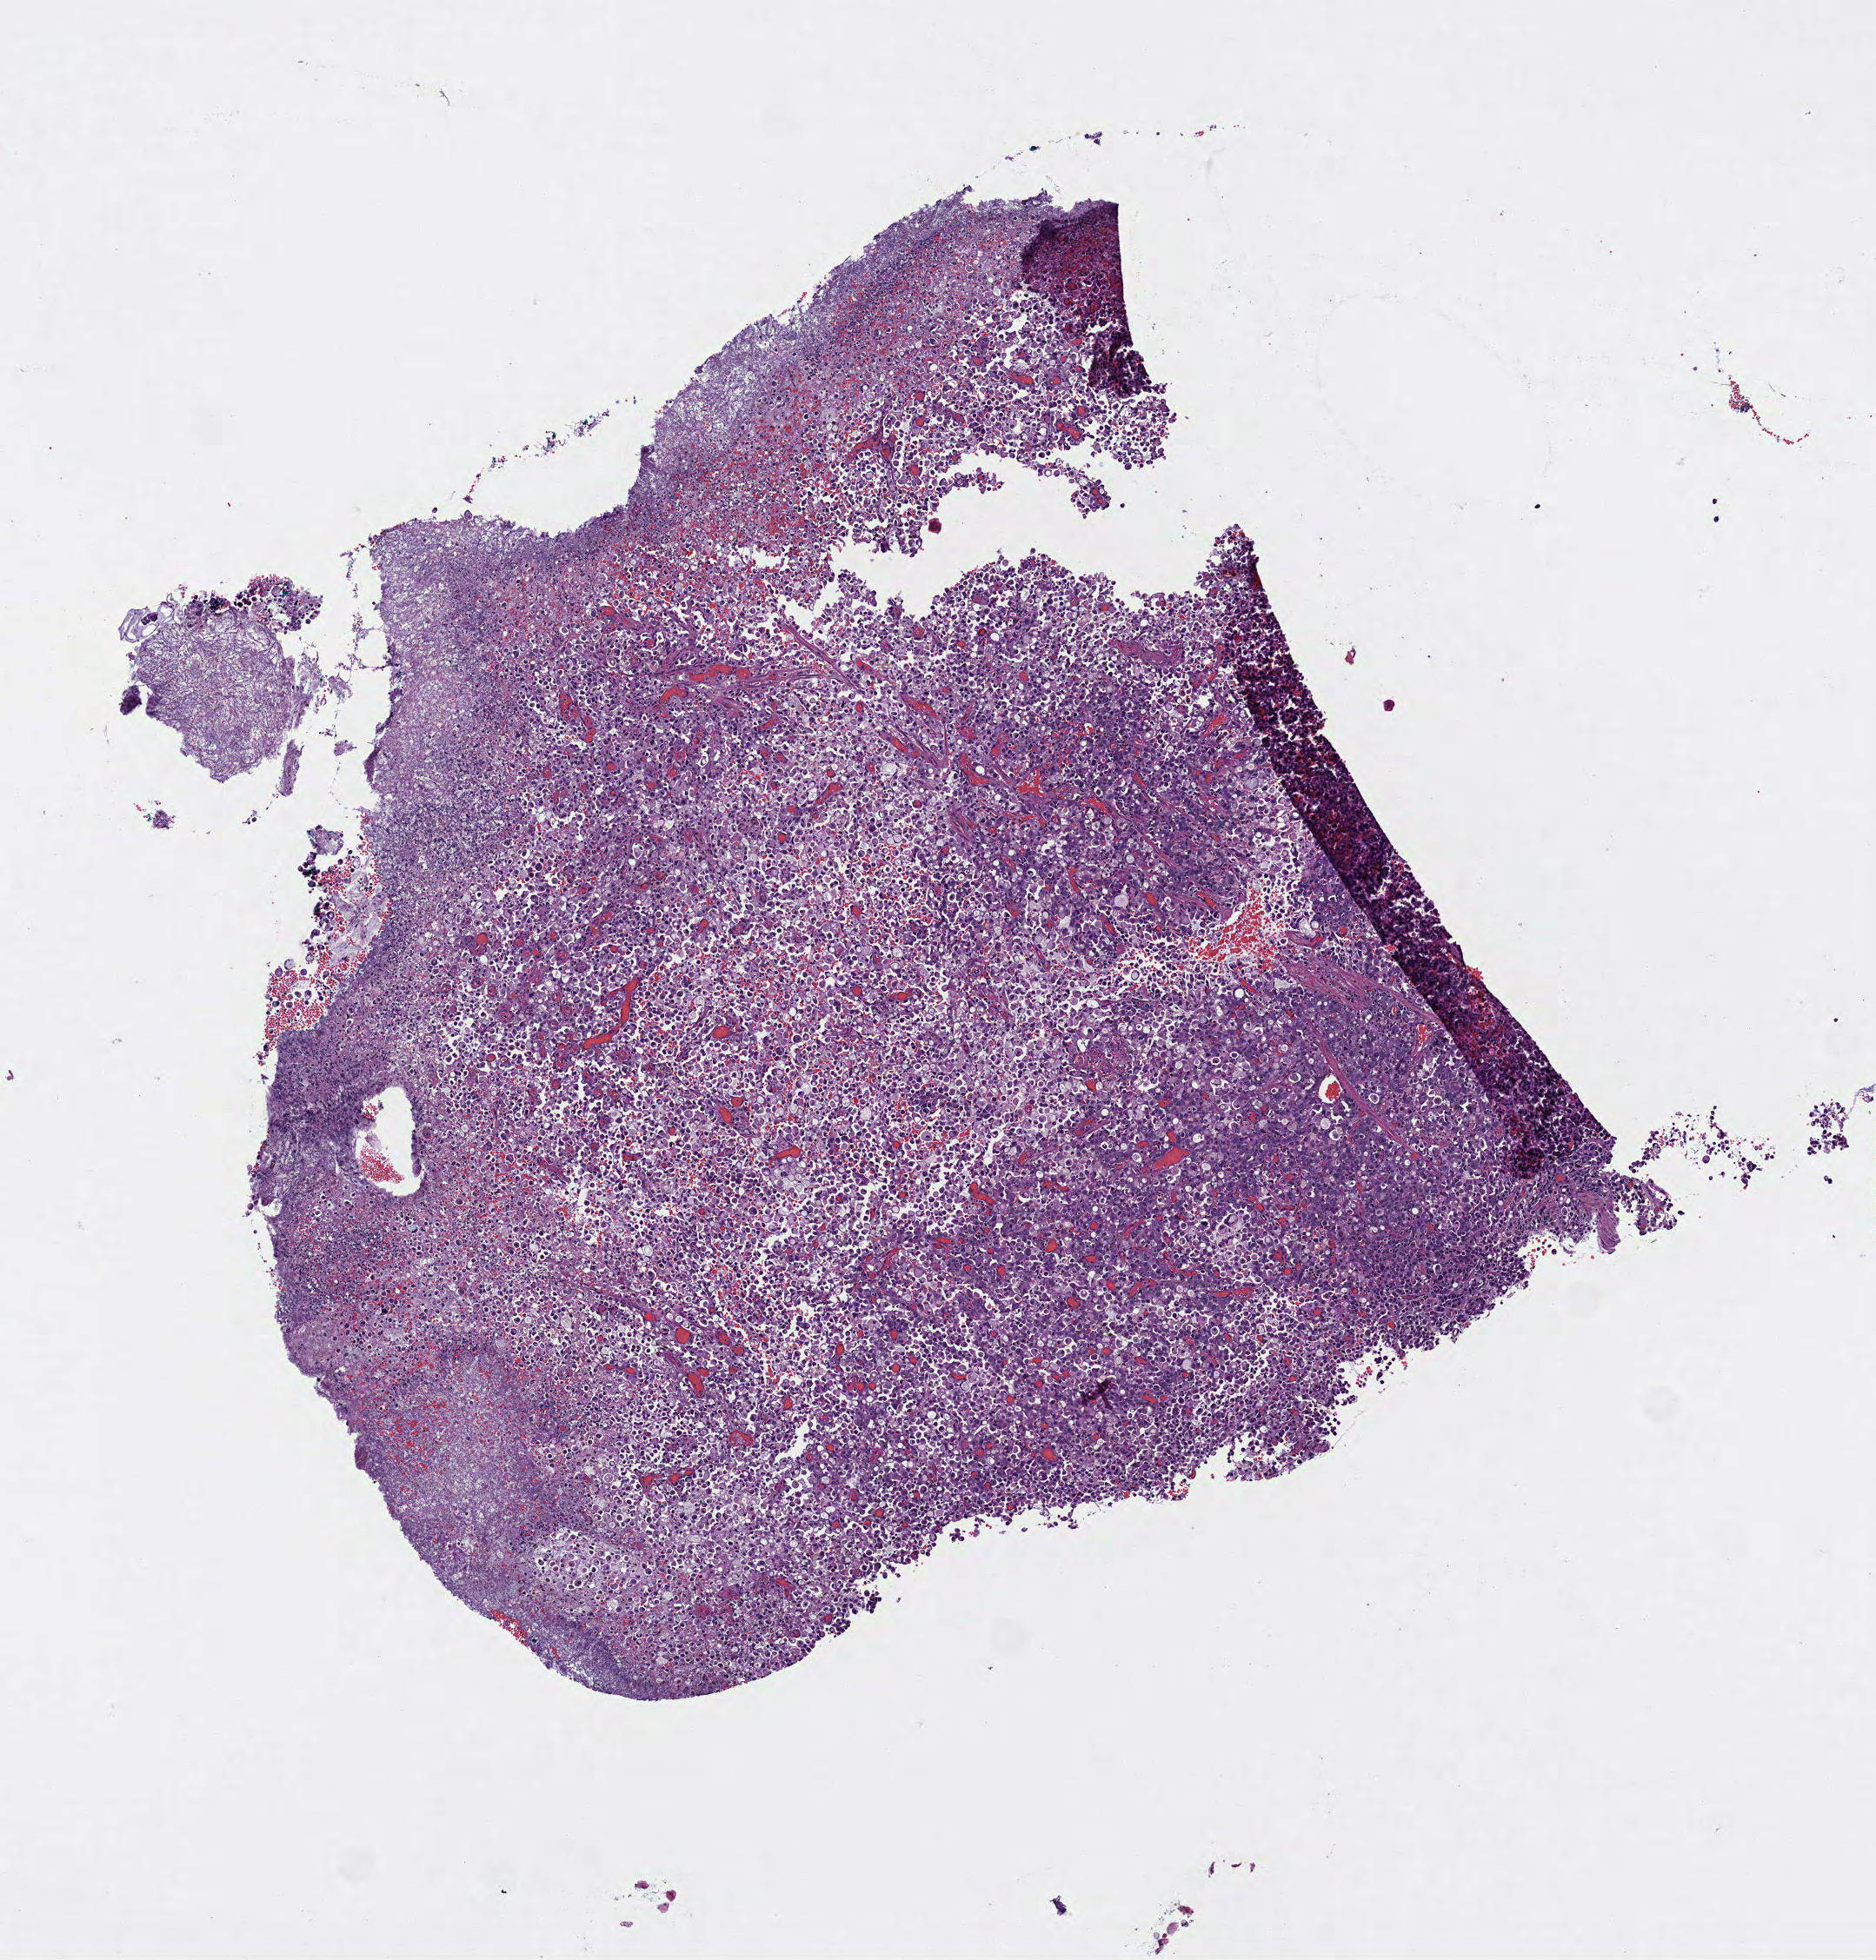
Hematoxylin and eosin (H&E) stained whole-slide image — whole scanned area (about 4.4 x 4.5 mm, slide scanned at 40x) shown as a low-resolution overview; formalin-fixed paraffin-embedded (FFPE) diagnostic section; sample: primary tumour, stomach. Patient: male, age at initial diagnosis 60 years. Histologic grade: G3 (poorly differentiated).
* AJCC pathologic stage: IIIC (7th edition)
* pathologic diagnosis: Signet ring cell carcinoma (body of stomach)
* TNM: T4b N3a MX